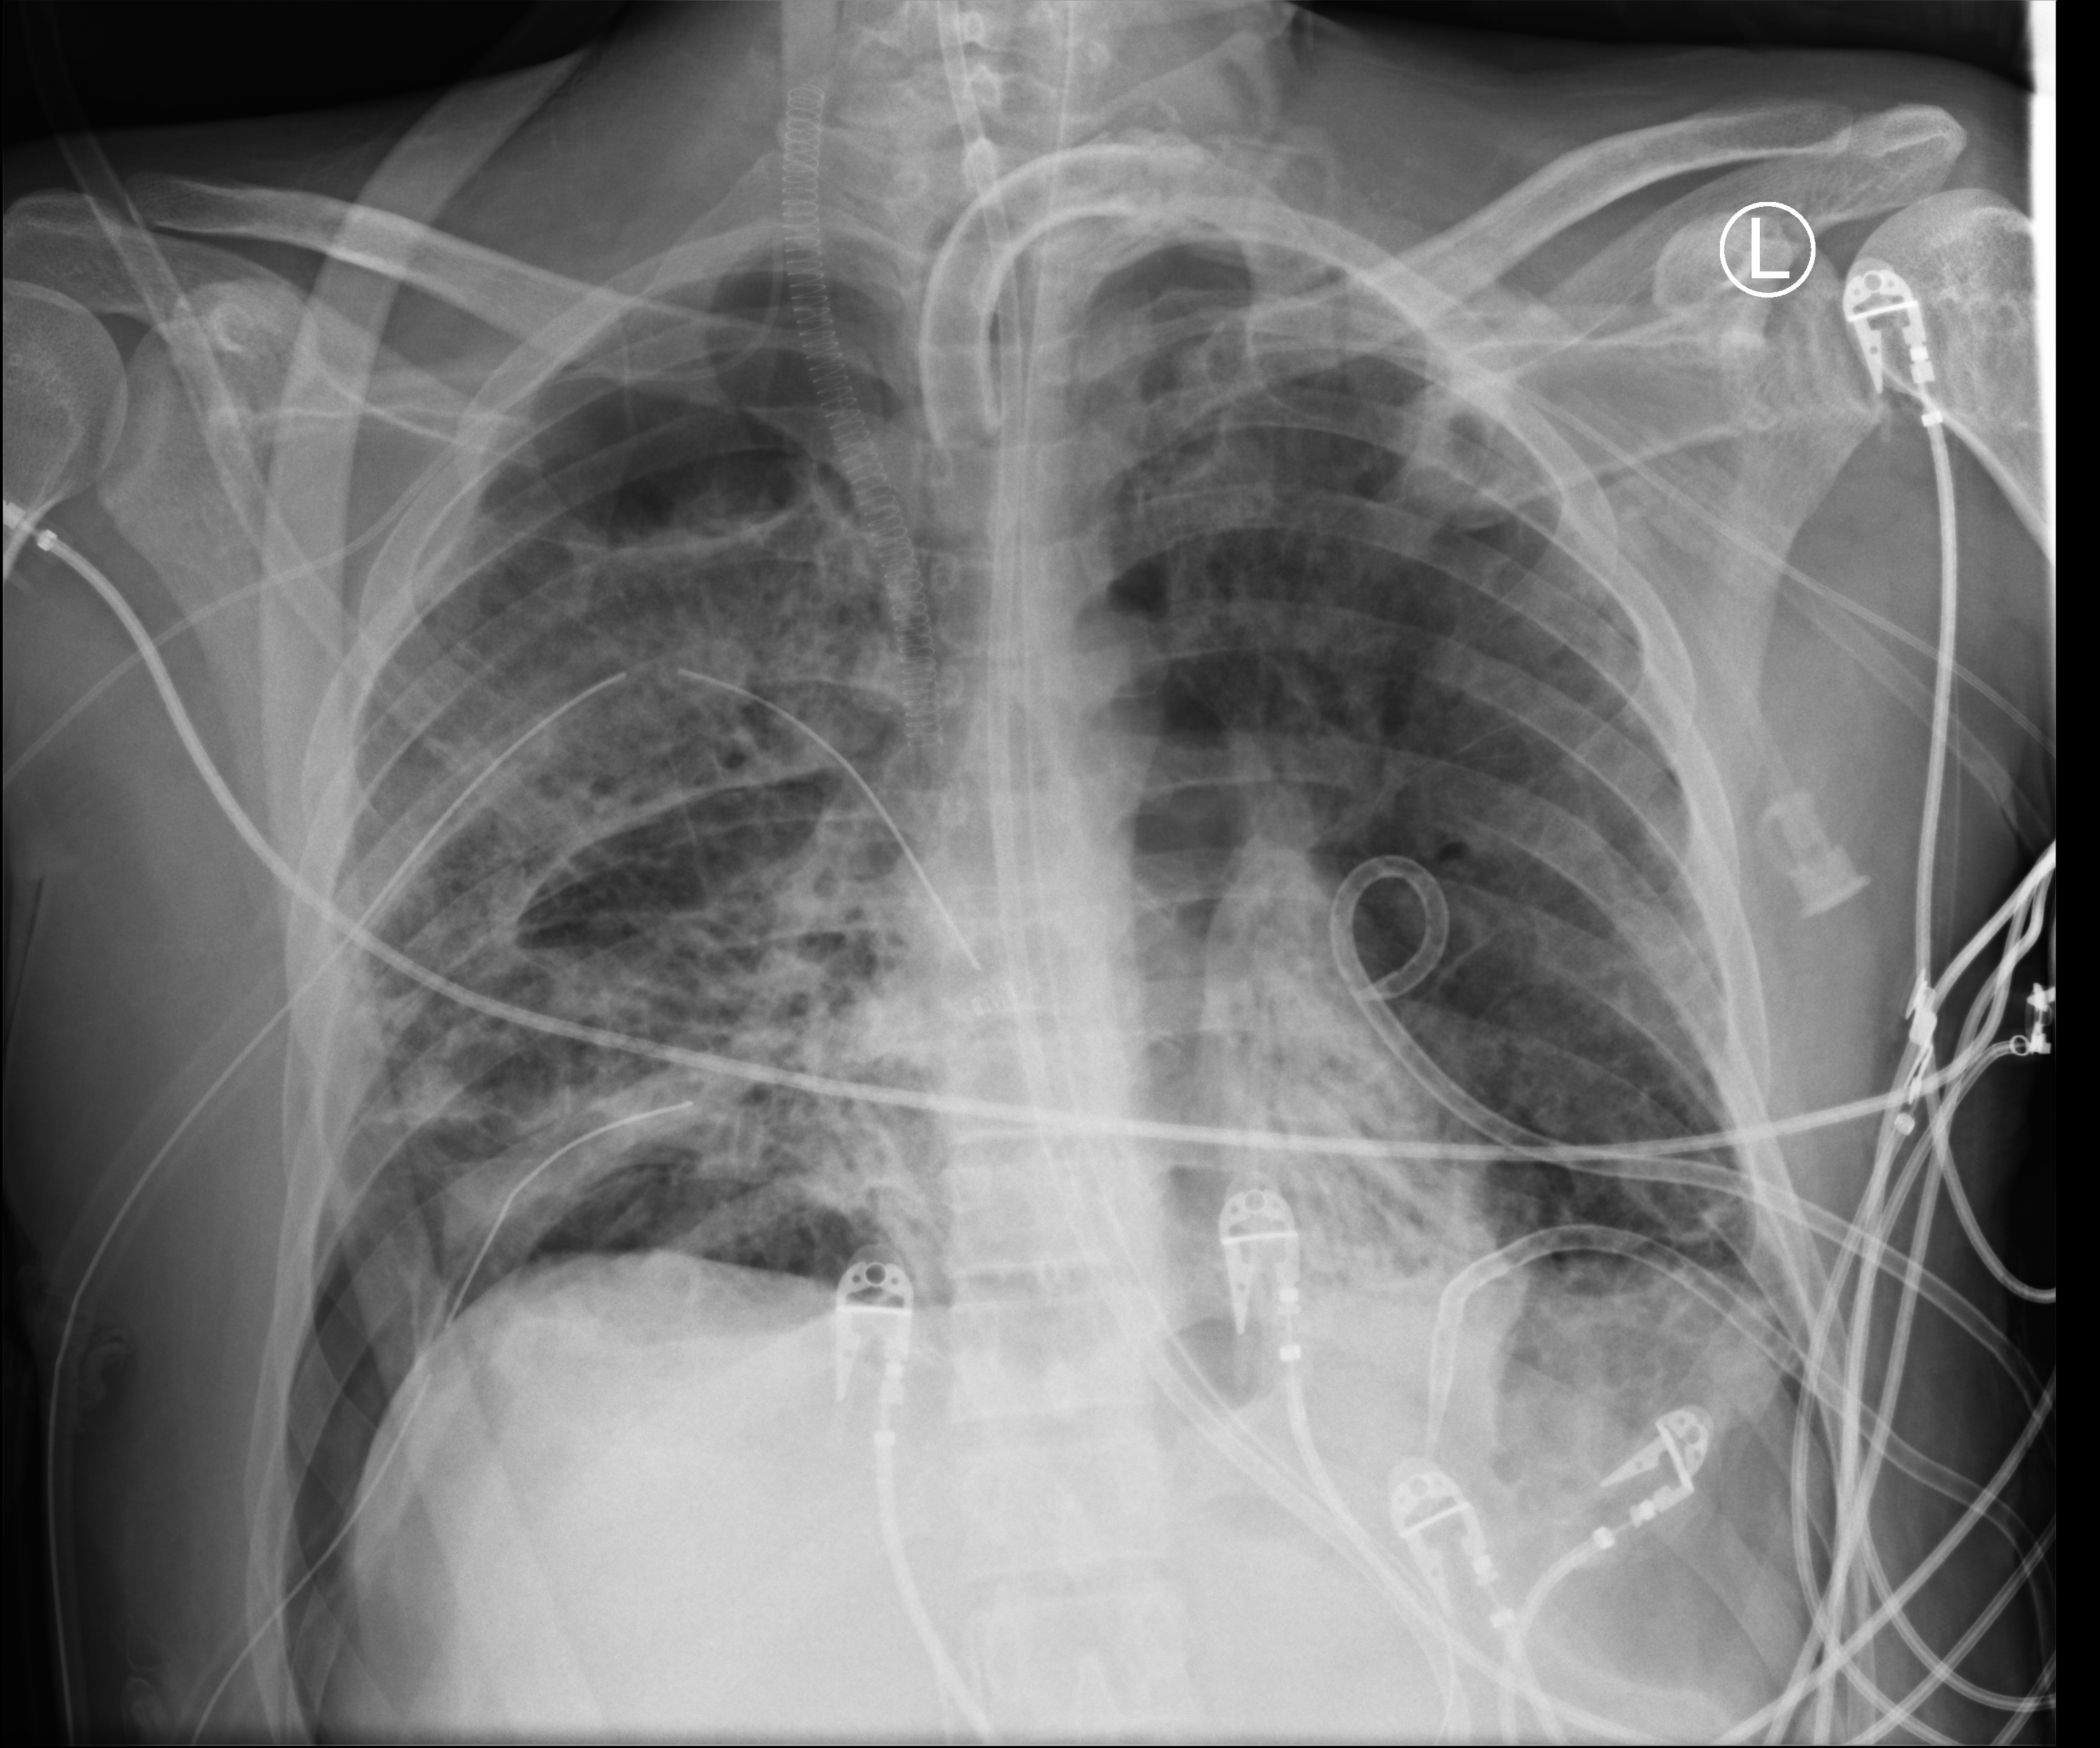
Bedside chest radiograph (computed radiography). Adult patient hospitalised with COVID-19, age 18–59 years.
Admission-level facts for this patient (not findings on this image; timing relative to this image not recorded): diabetes (admission record): no; admitted to intensive care during this hospital stay: yes.